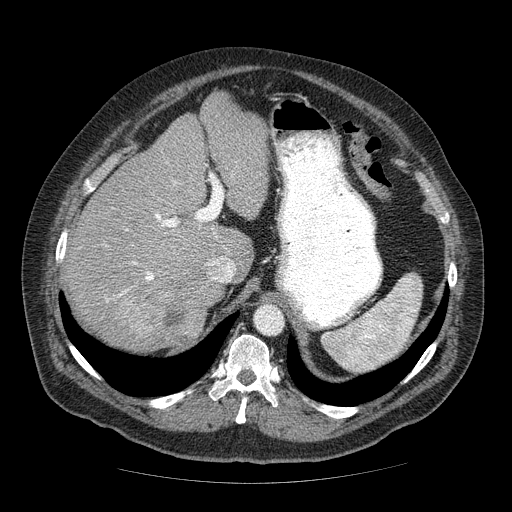
Contrast-enhanced abdominal CT (liver protocol), one axial slice. Position 44 of 85 along the scan axis. Soft-tissue window (W 400 / L 40 HU). 512 × 512 image matrix. Case-level facts recorded for this patient, not image findings: diagnosis: hepatocellular carcinoma (patient treated with transarterial chemoembolisation; whether this scan precedes or follows treatment is not stated here); TNM stage (as recorded): Stage-IIIA; Child-Pugh class: A.
Outlined on this slice (semi-automatically segmented with operator editing):
- liver parenchyma outside the tumour (the mass and vessels are separate outlines, so this box may not span the whole liver): bounding box (x1, y1, x2, y2) in pixels: (64, 94, 268, 350)
- mass: (103, 278, 221, 349)
- liver vessels: (106, 182, 179, 302)